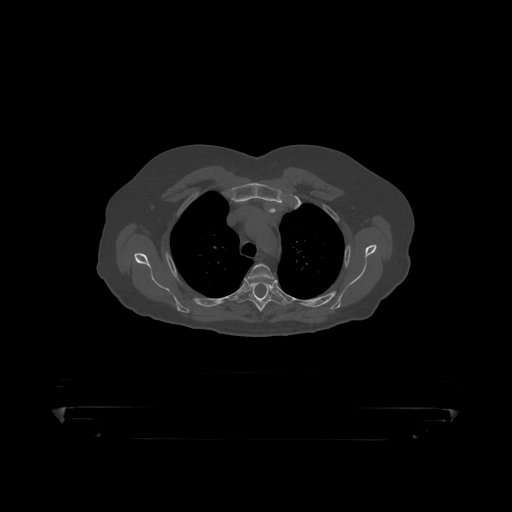
CT including the spine, one axial slice; slice 345 of 390 in the series (ordered by position); reconstruction kernel STANDARD; bone window (W 1800 / L 400 HU); 1.25 mm slice thickness; 512 × 512 image matrix. Patient: male, 60 years. Case-level facts recorded for this patient, not image findings: primary cancer: prostate.
Outlined on this slice (semi-automatic segmentation, software-assisted and operator-edited):
- T3 vertebra: bounding box (x1, y1, x2, y2) in pixels: (248, 264, 275, 287)
- T4 vertebra: (237, 284, 285, 313)